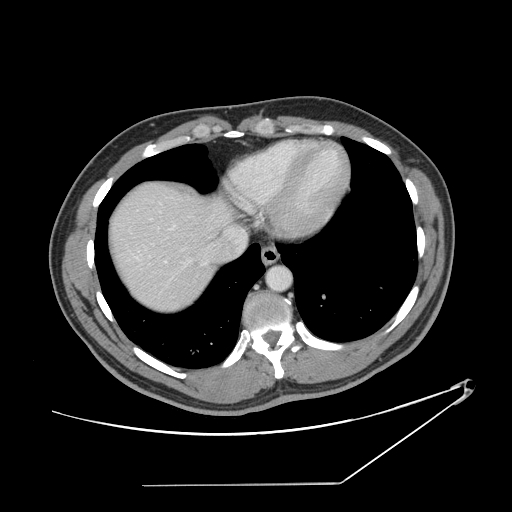
Contrast-enhanced abdominal CT, one axial slice; slice 131 of 152 in the series (ordered by position); reconstruction kernel STANDARD; intravenous contrast given; soft-tissue window (W 400 / L 40 HU); 2.5 mm slice thickness; 512 × 512 image matrix, field of view 432 × 432 mm. Male patient, age 45 years. Case-level facts recorded for this patient, not image findings: diagnosis: colorectal cancer liver metastases, imaged before liver resection; multiple liver metastases: no; largest metastasis: 1 cm; disease in both lobes: no.
Structures marked on this image (outlined manually by an expert reader):
- hepatic veins: bounding box (x1, y1, x2, y2) in pixels: (137, 203, 244, 264)
- liver: (112, 184, 227, 310)
- planned liver remnant (the part of the liver to remain after resection): (112, 185, 227, 310)